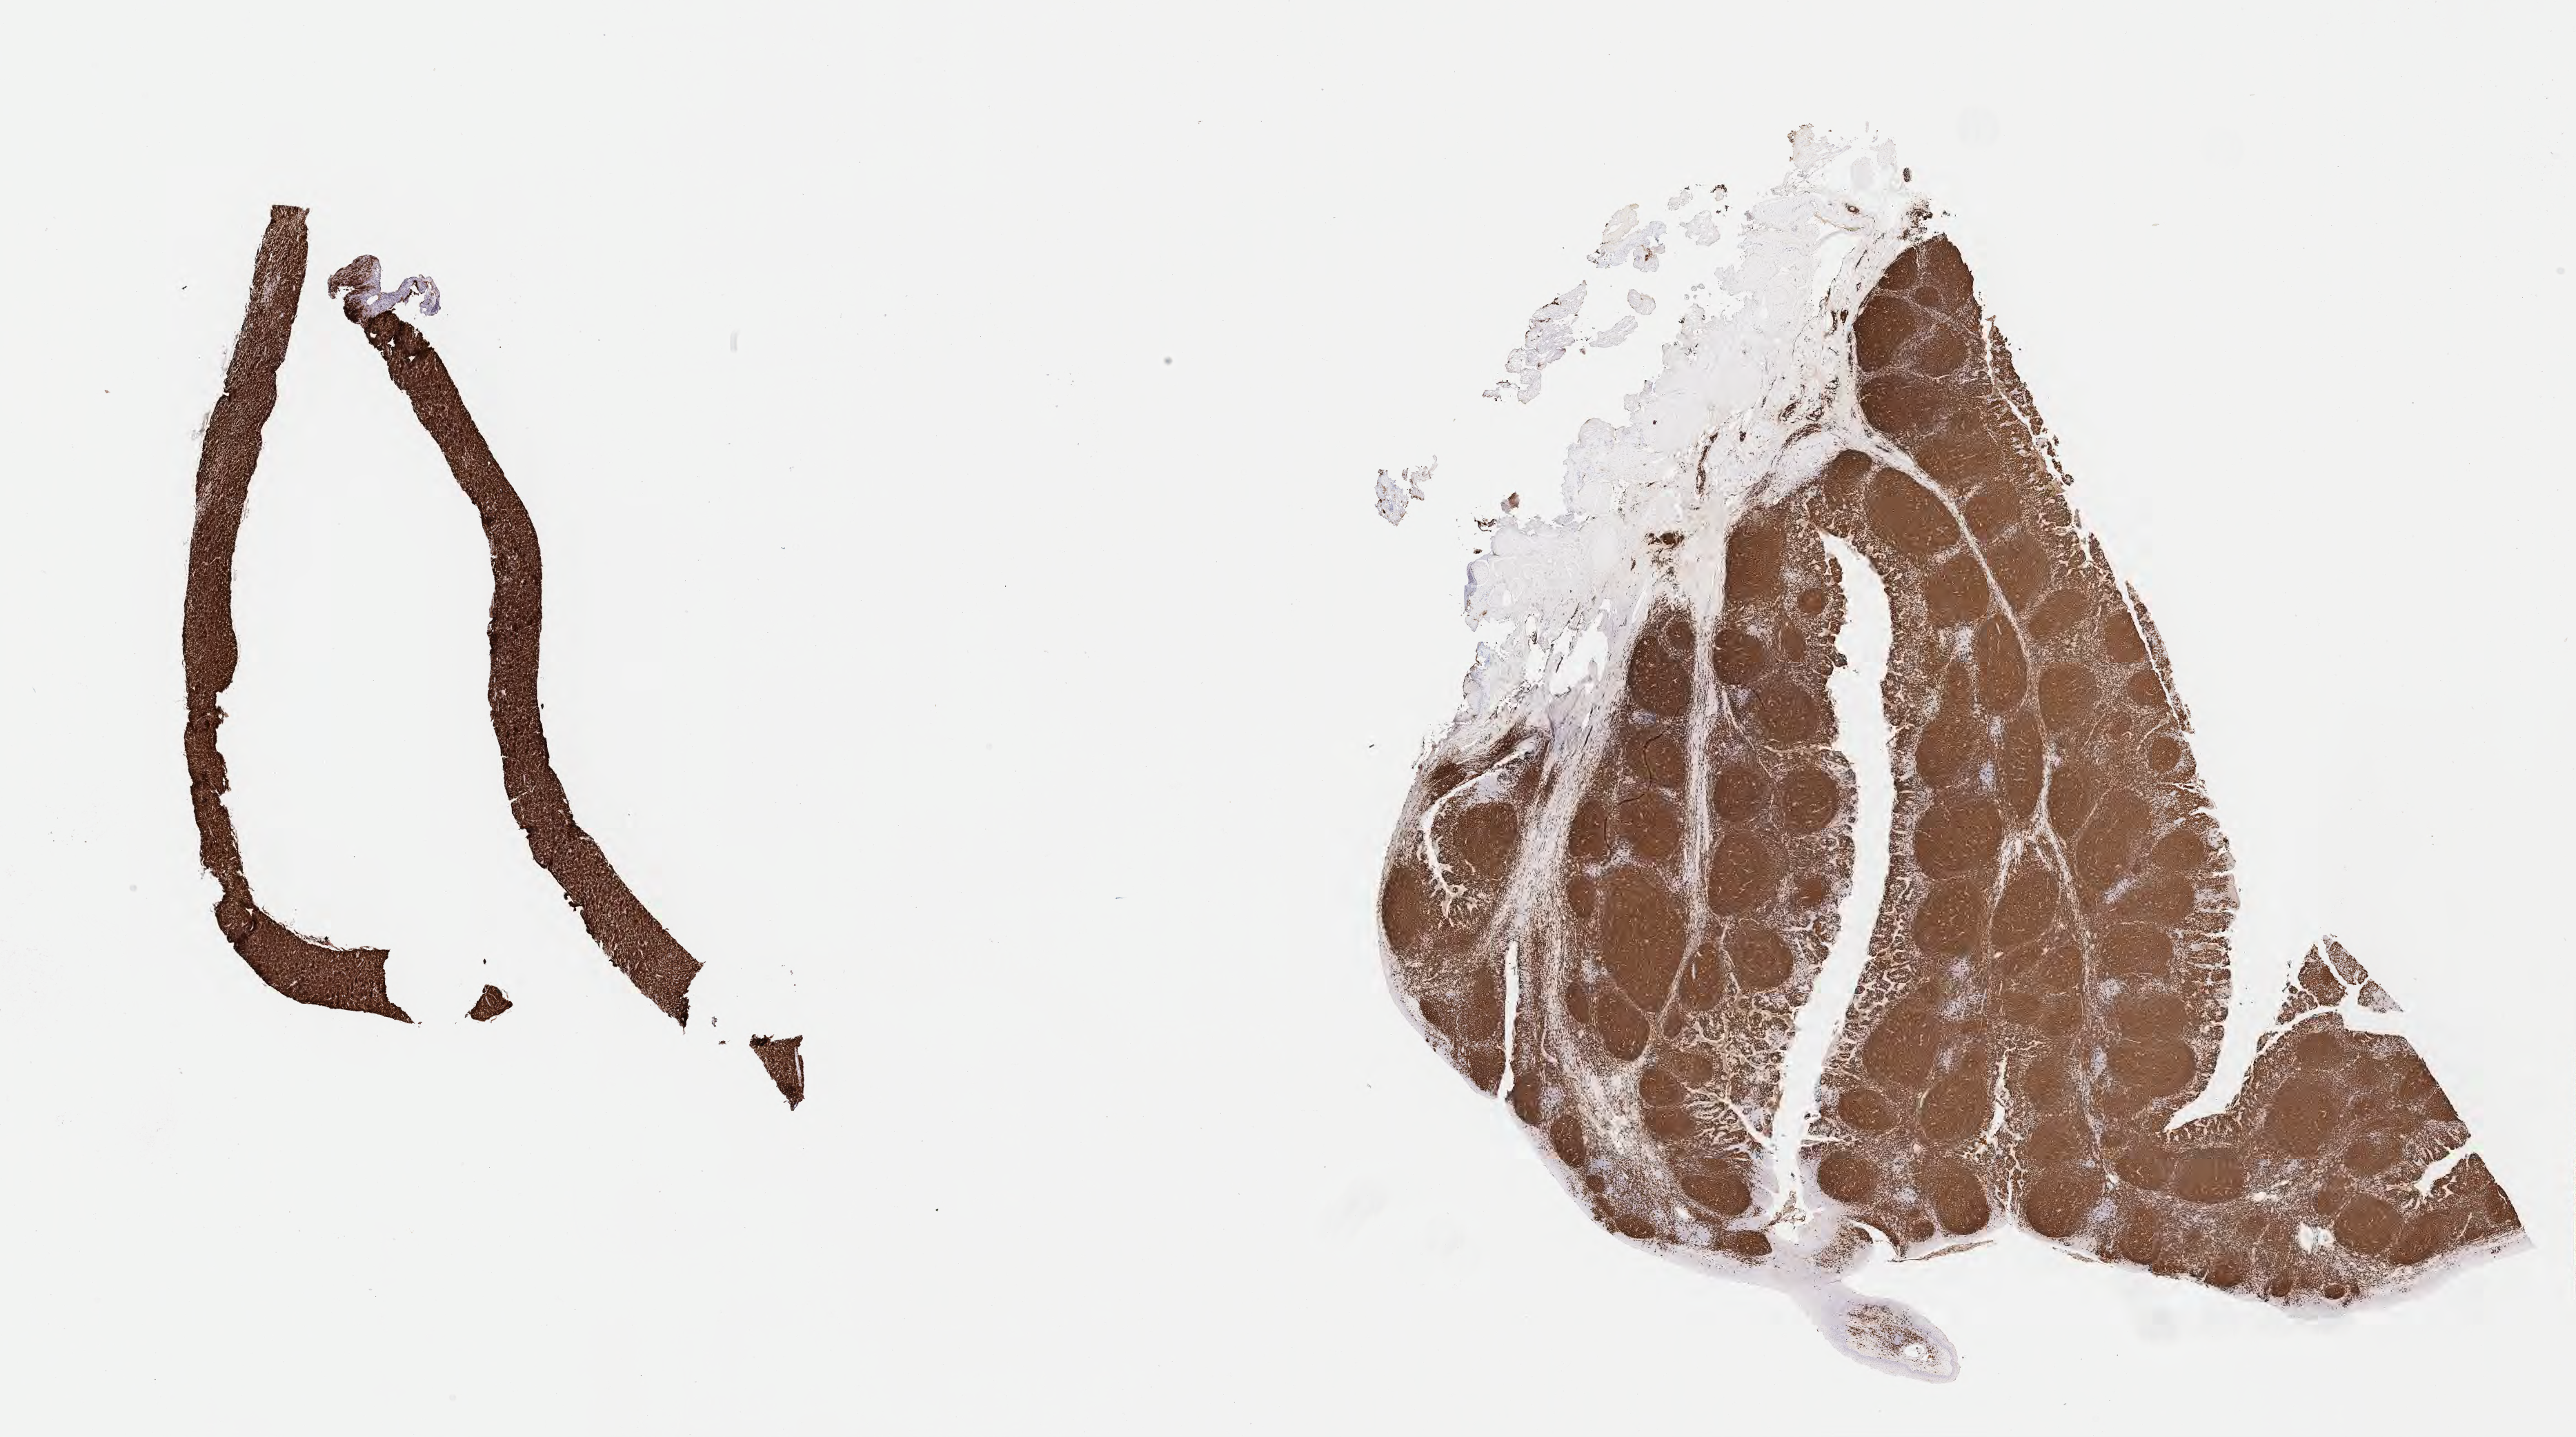
Whole-slide image, immunohistochemical stain for CD20, shown as a low-resolution overview of the whole scanned area (about 30.2 x 16.8 mm). Specimen: tumor tissue. Site: abdomen proper. Male patient; age at initial diagnosis 9 years.
Histologic diagnosis: Burkitt lymphoma, NOS.